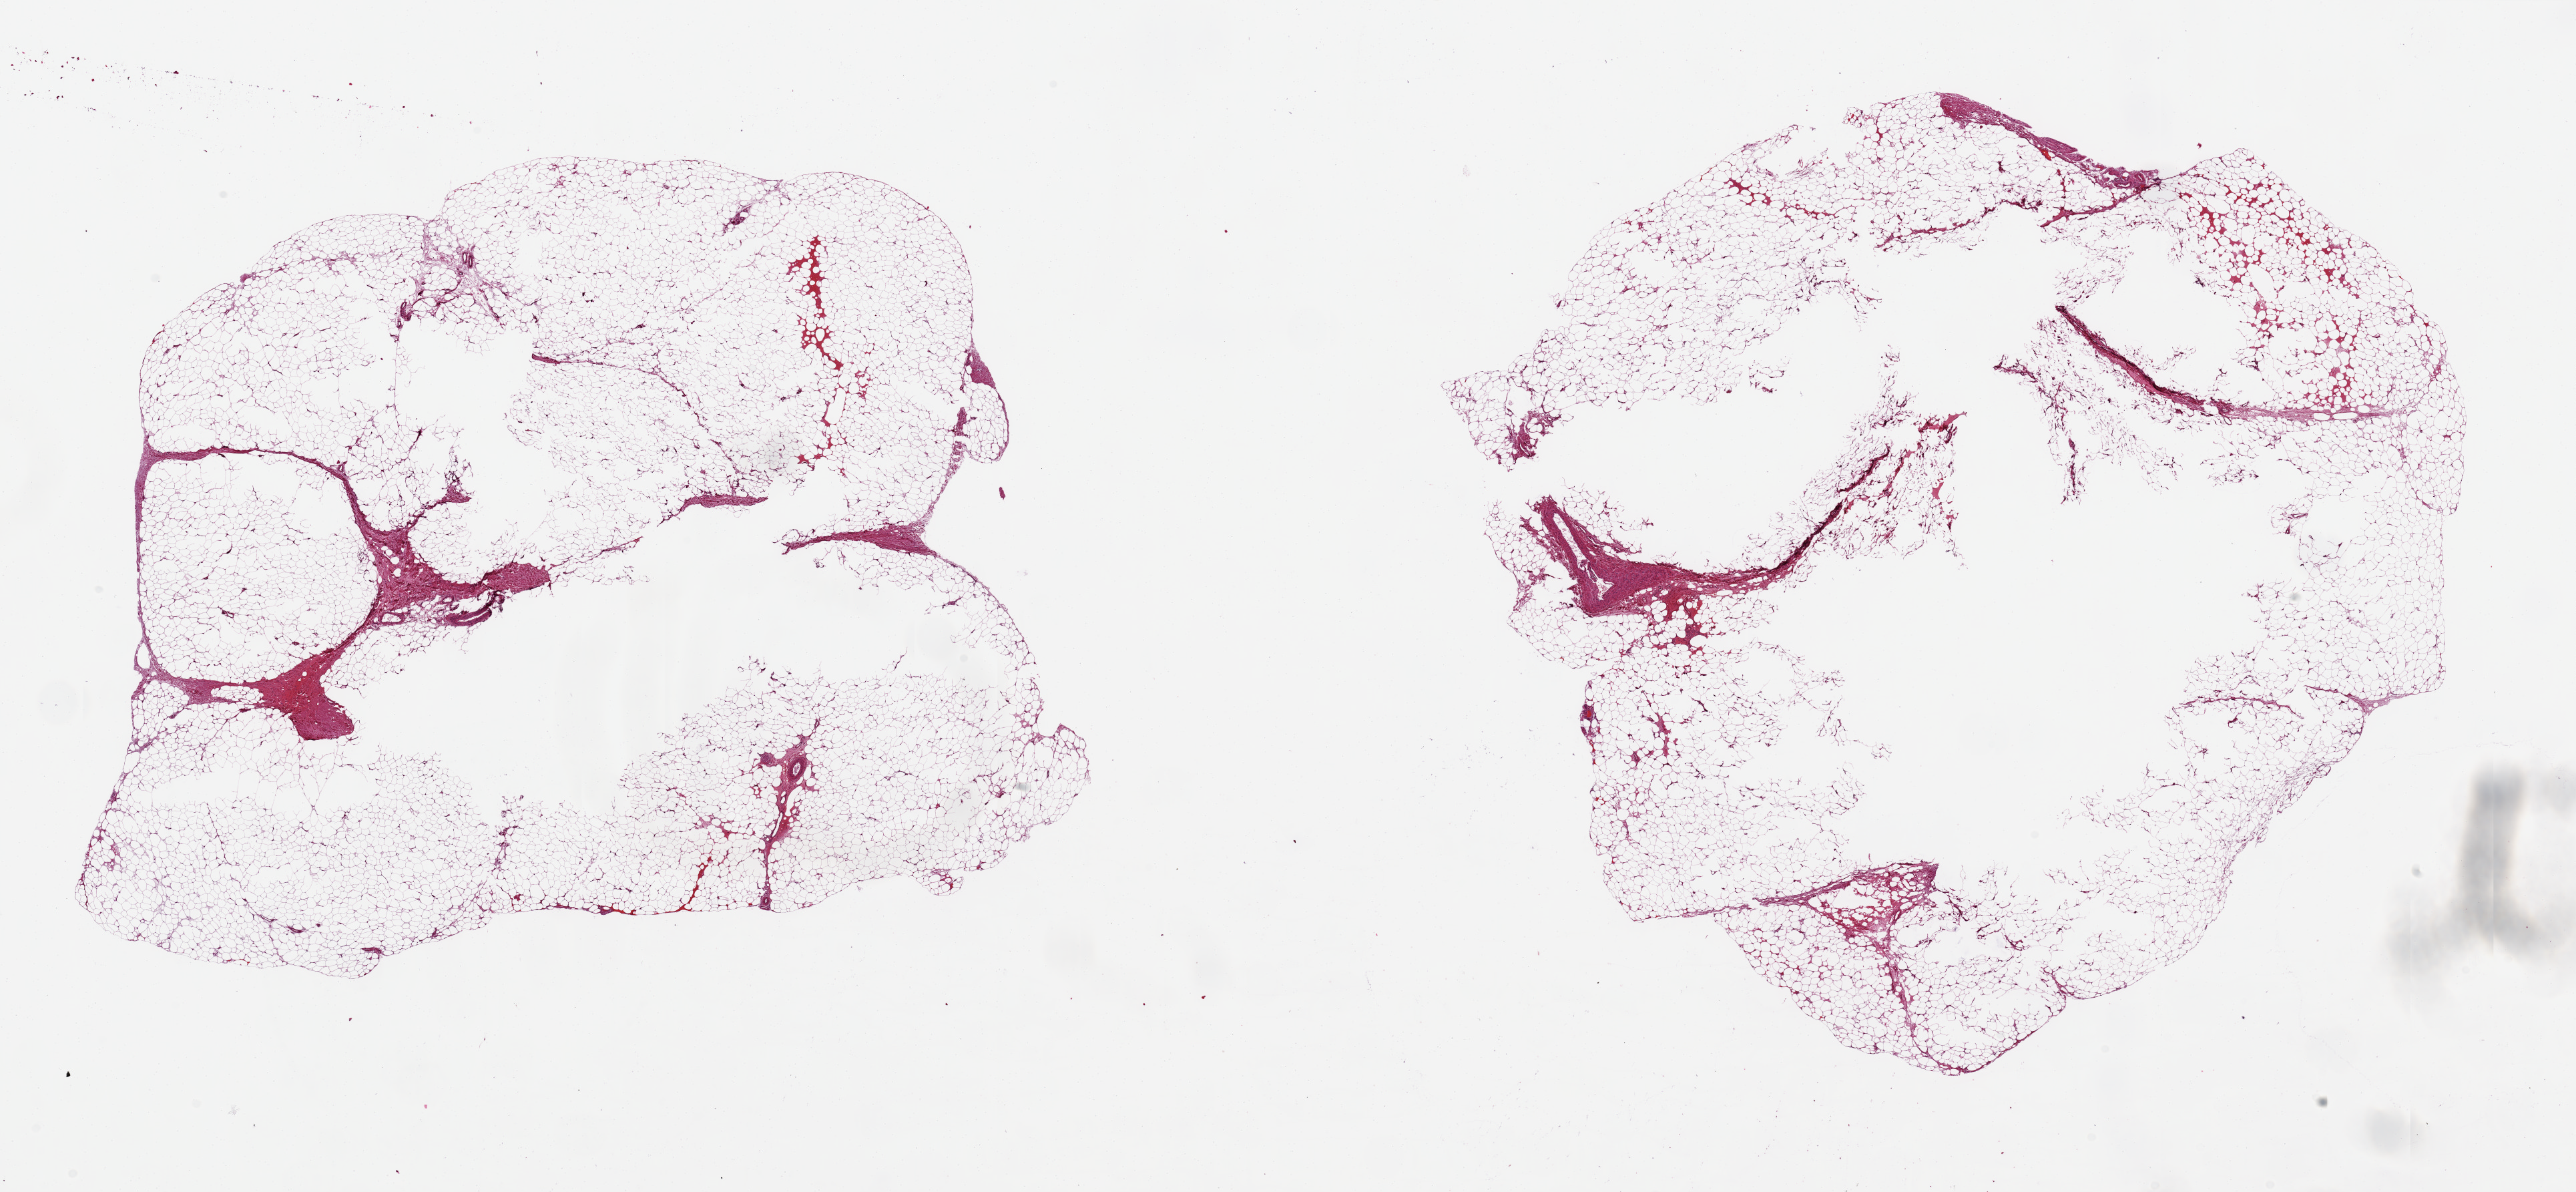
H&E whole-slide image, brightfield — whole scanned area (about 30.5 x 14.1 mm, slide scanned at 20x) shown as a low-resolution overview, PAXgene-fixed paraffin-embedded (PFPE) section, section of adipose tissue (target tissue), tissue donor sample. Female donor.
Pathologist's review note for this sample: 2 large pieces, 9x11 and 10x11 mm. Both with large empty central areas of under-fixation.